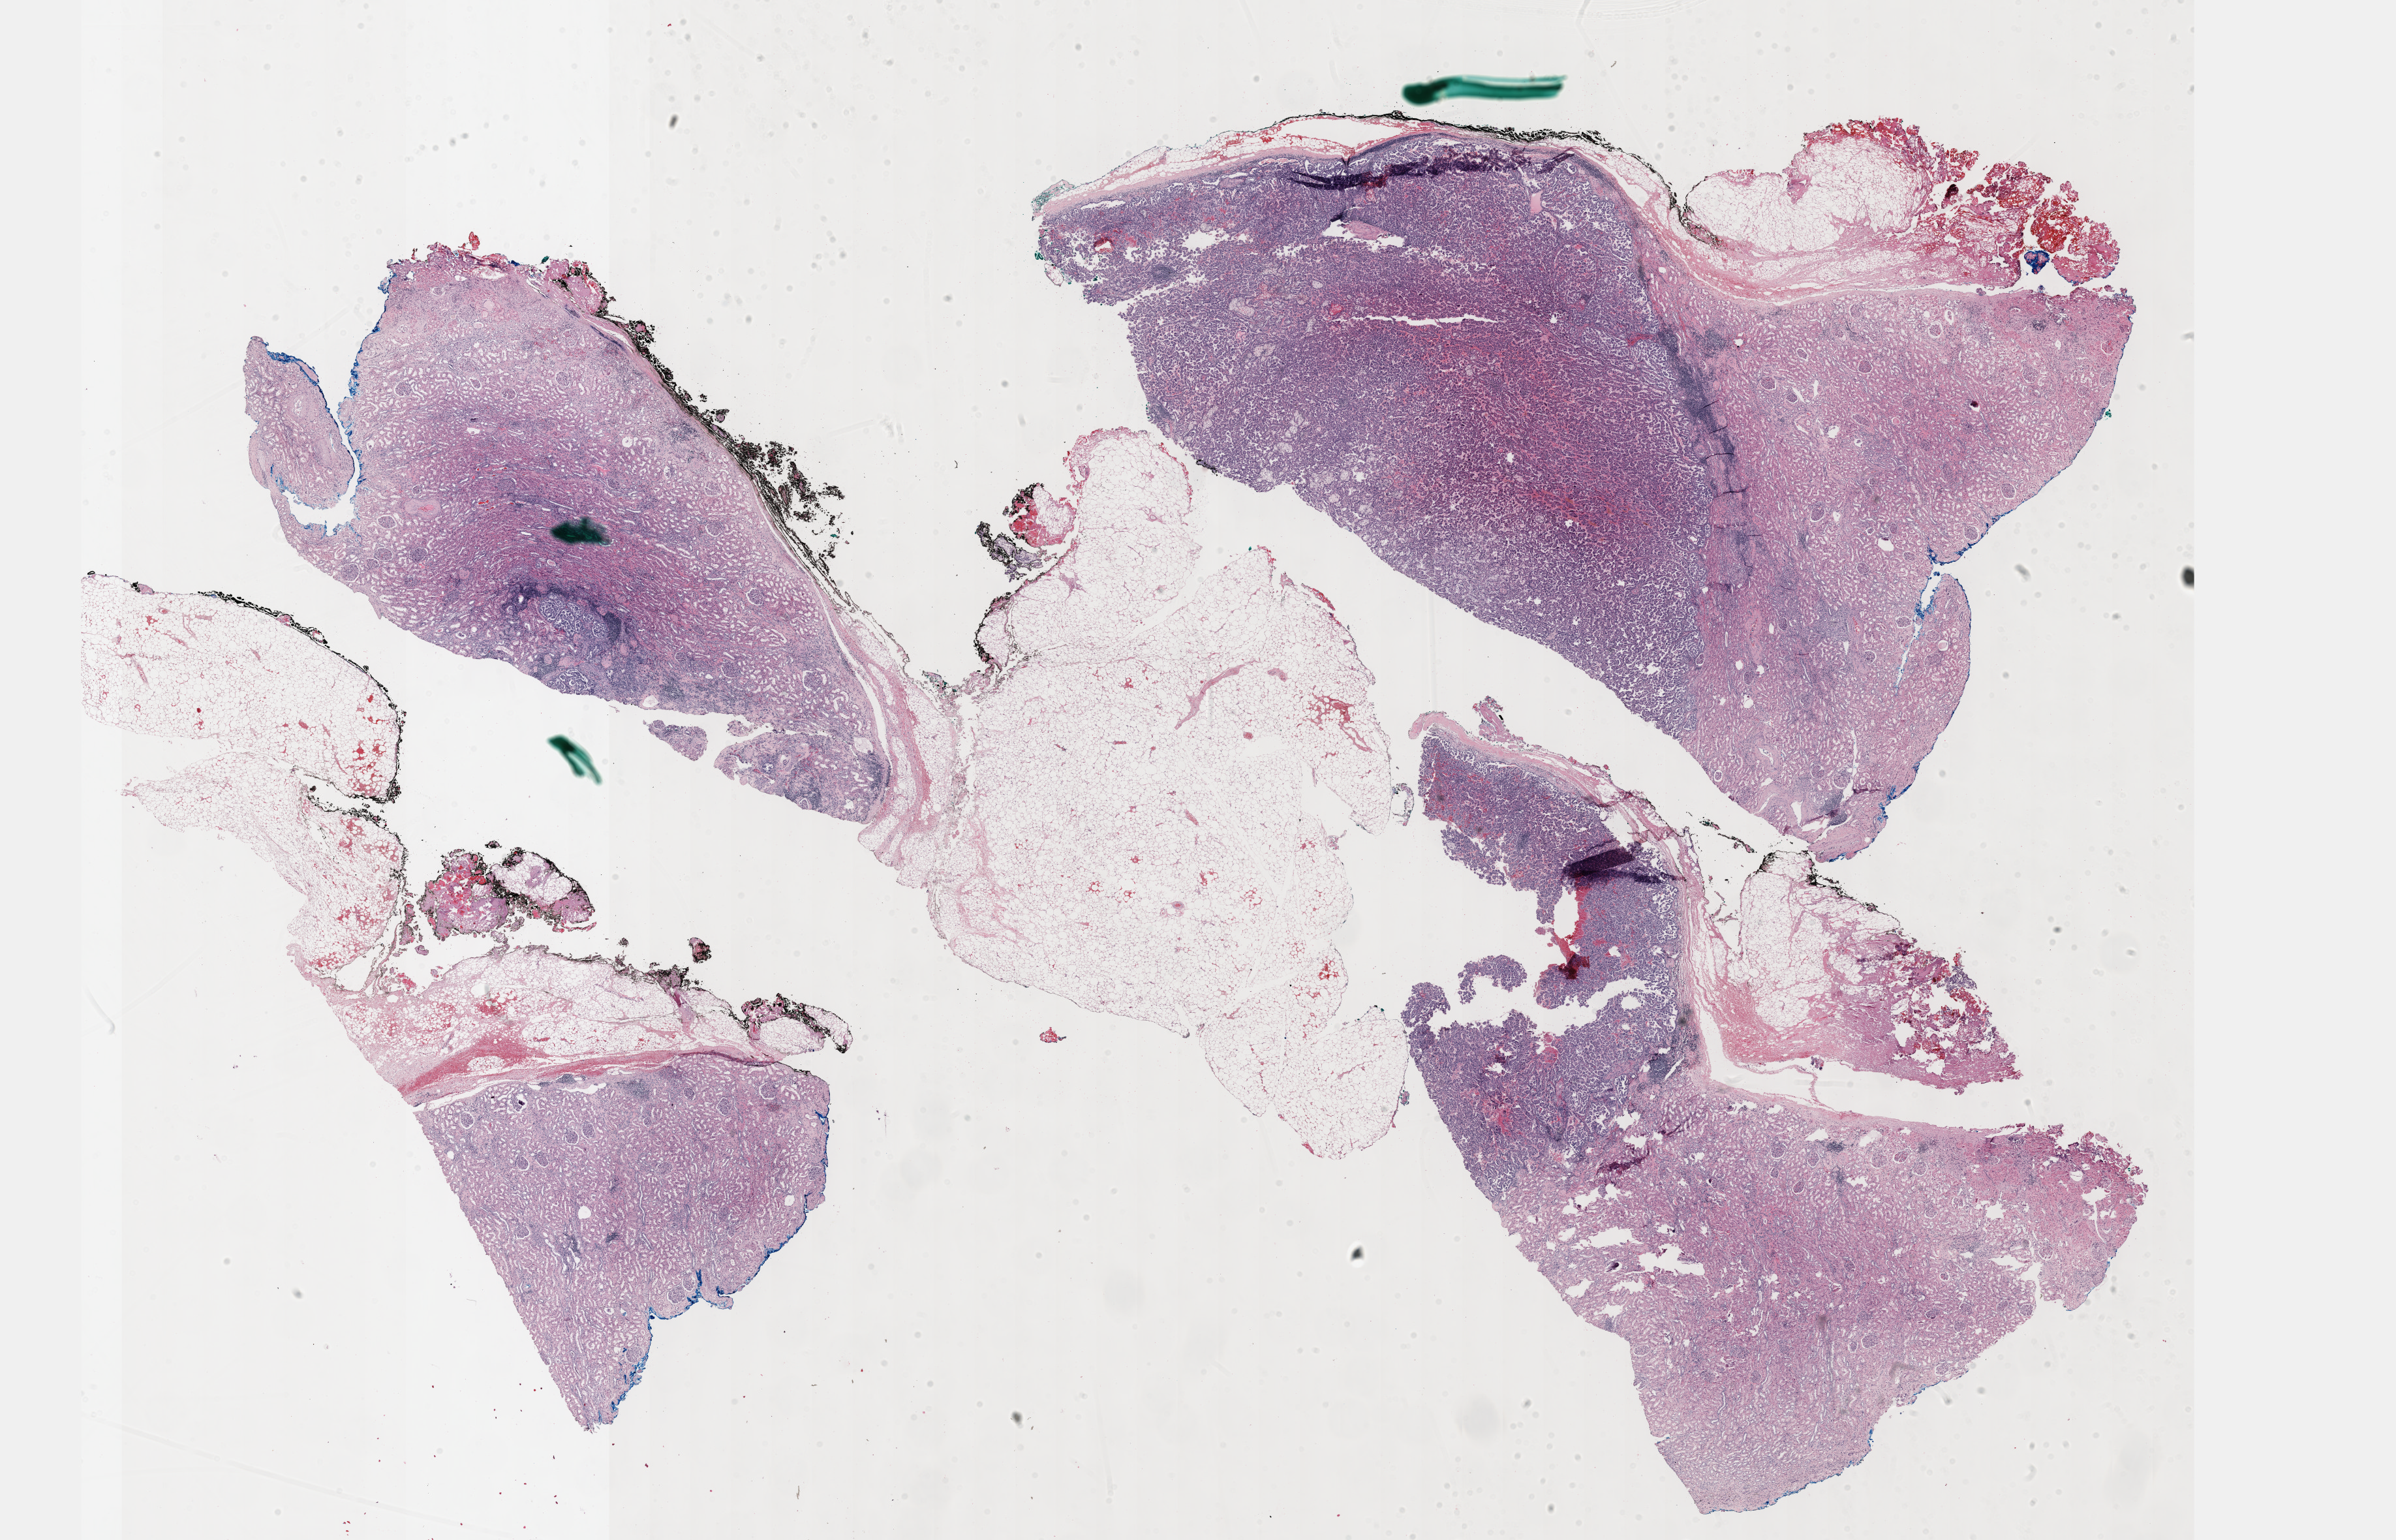
Hematoxylin and eosin (H&E) stained whole-slide image, whole scanned area (about 29.7 x 19.1 mm, from a 40x scan) shown as a low-resolution overview. Formalin-fixed paraffin-embedded (FFPE) diagnostic section. Sample: primary tumour, kidney. Male, age 65 years at initial diagnosis.
• AJCC pathologic stage: I (7th edition)
• histologic diagnosis: Papillary adenocarcinoma, NOS